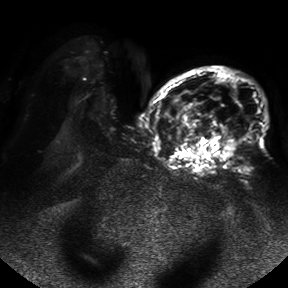
Breast MRI, one axial slice; slice 28 of 50 in the series (ordered by position); diffusion-weighted series; image 2 of 4 stored at this slice position (different b-values; order by instance number); 1.5 T; 4 mm slice thickness; 288 × 288 image matrix. Female patient.
Structures marked on this image (outlined manually by an expert reader):
- tumour on diffusion-weighted imaging: box from (x=166, y=97) to (x=237, y=156) px